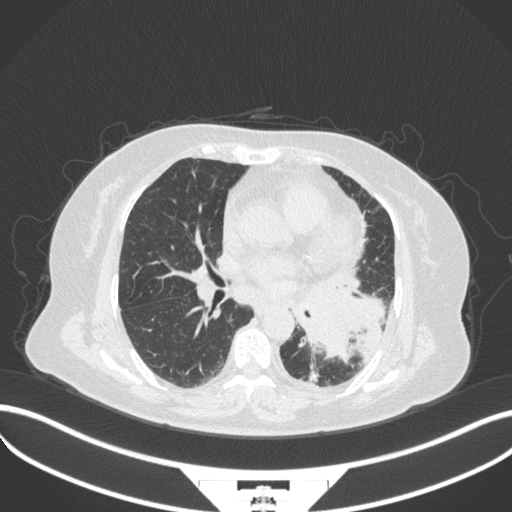
Chest CT, one axial slice. Position 173 of 328 along the scan axis. Reconstruction kernel B31f. 120 kVp. Lung window (W 1500 / L -600 HU). 512 × 512 image matrix. Female patient, age 69 years. Case-level facts recorded for this patient, not image findings: clinical TNM (as recorded): T2b N3 M1.
Annotated regions visible in this slice (bounding box drawn by a radiologist):
- lung tumour (recorded histology: adenocarcinoma): box from (x=297, y=284) to (x=386, y=362) px